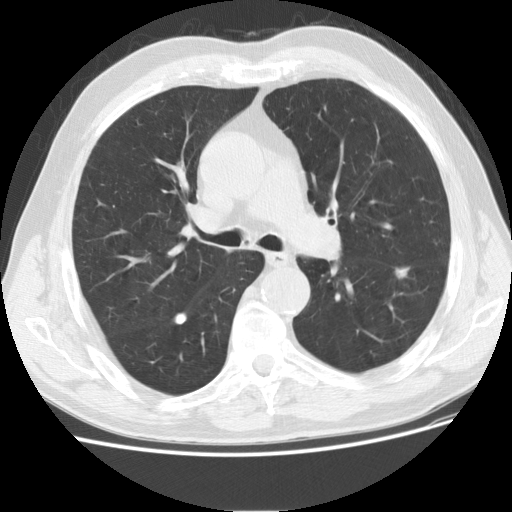
Low-dose screening chest CT, one axial slice. Slice 113 of 175 in the series (ordered by position). Reconstruction kernel STANDARD. Lung window (W 1500 / L -600 HU). 2.5 mm slice thickness. 512 × 512 image matrix, field of view 360 × 360 mm.
Outlined on this slice (outlined manually by an expert reader):
- lesion 1 (tumor, lower lobe of left lung): bounding box (x1, y1, x2, y2) in pixels: (395, 267, 410, 278)